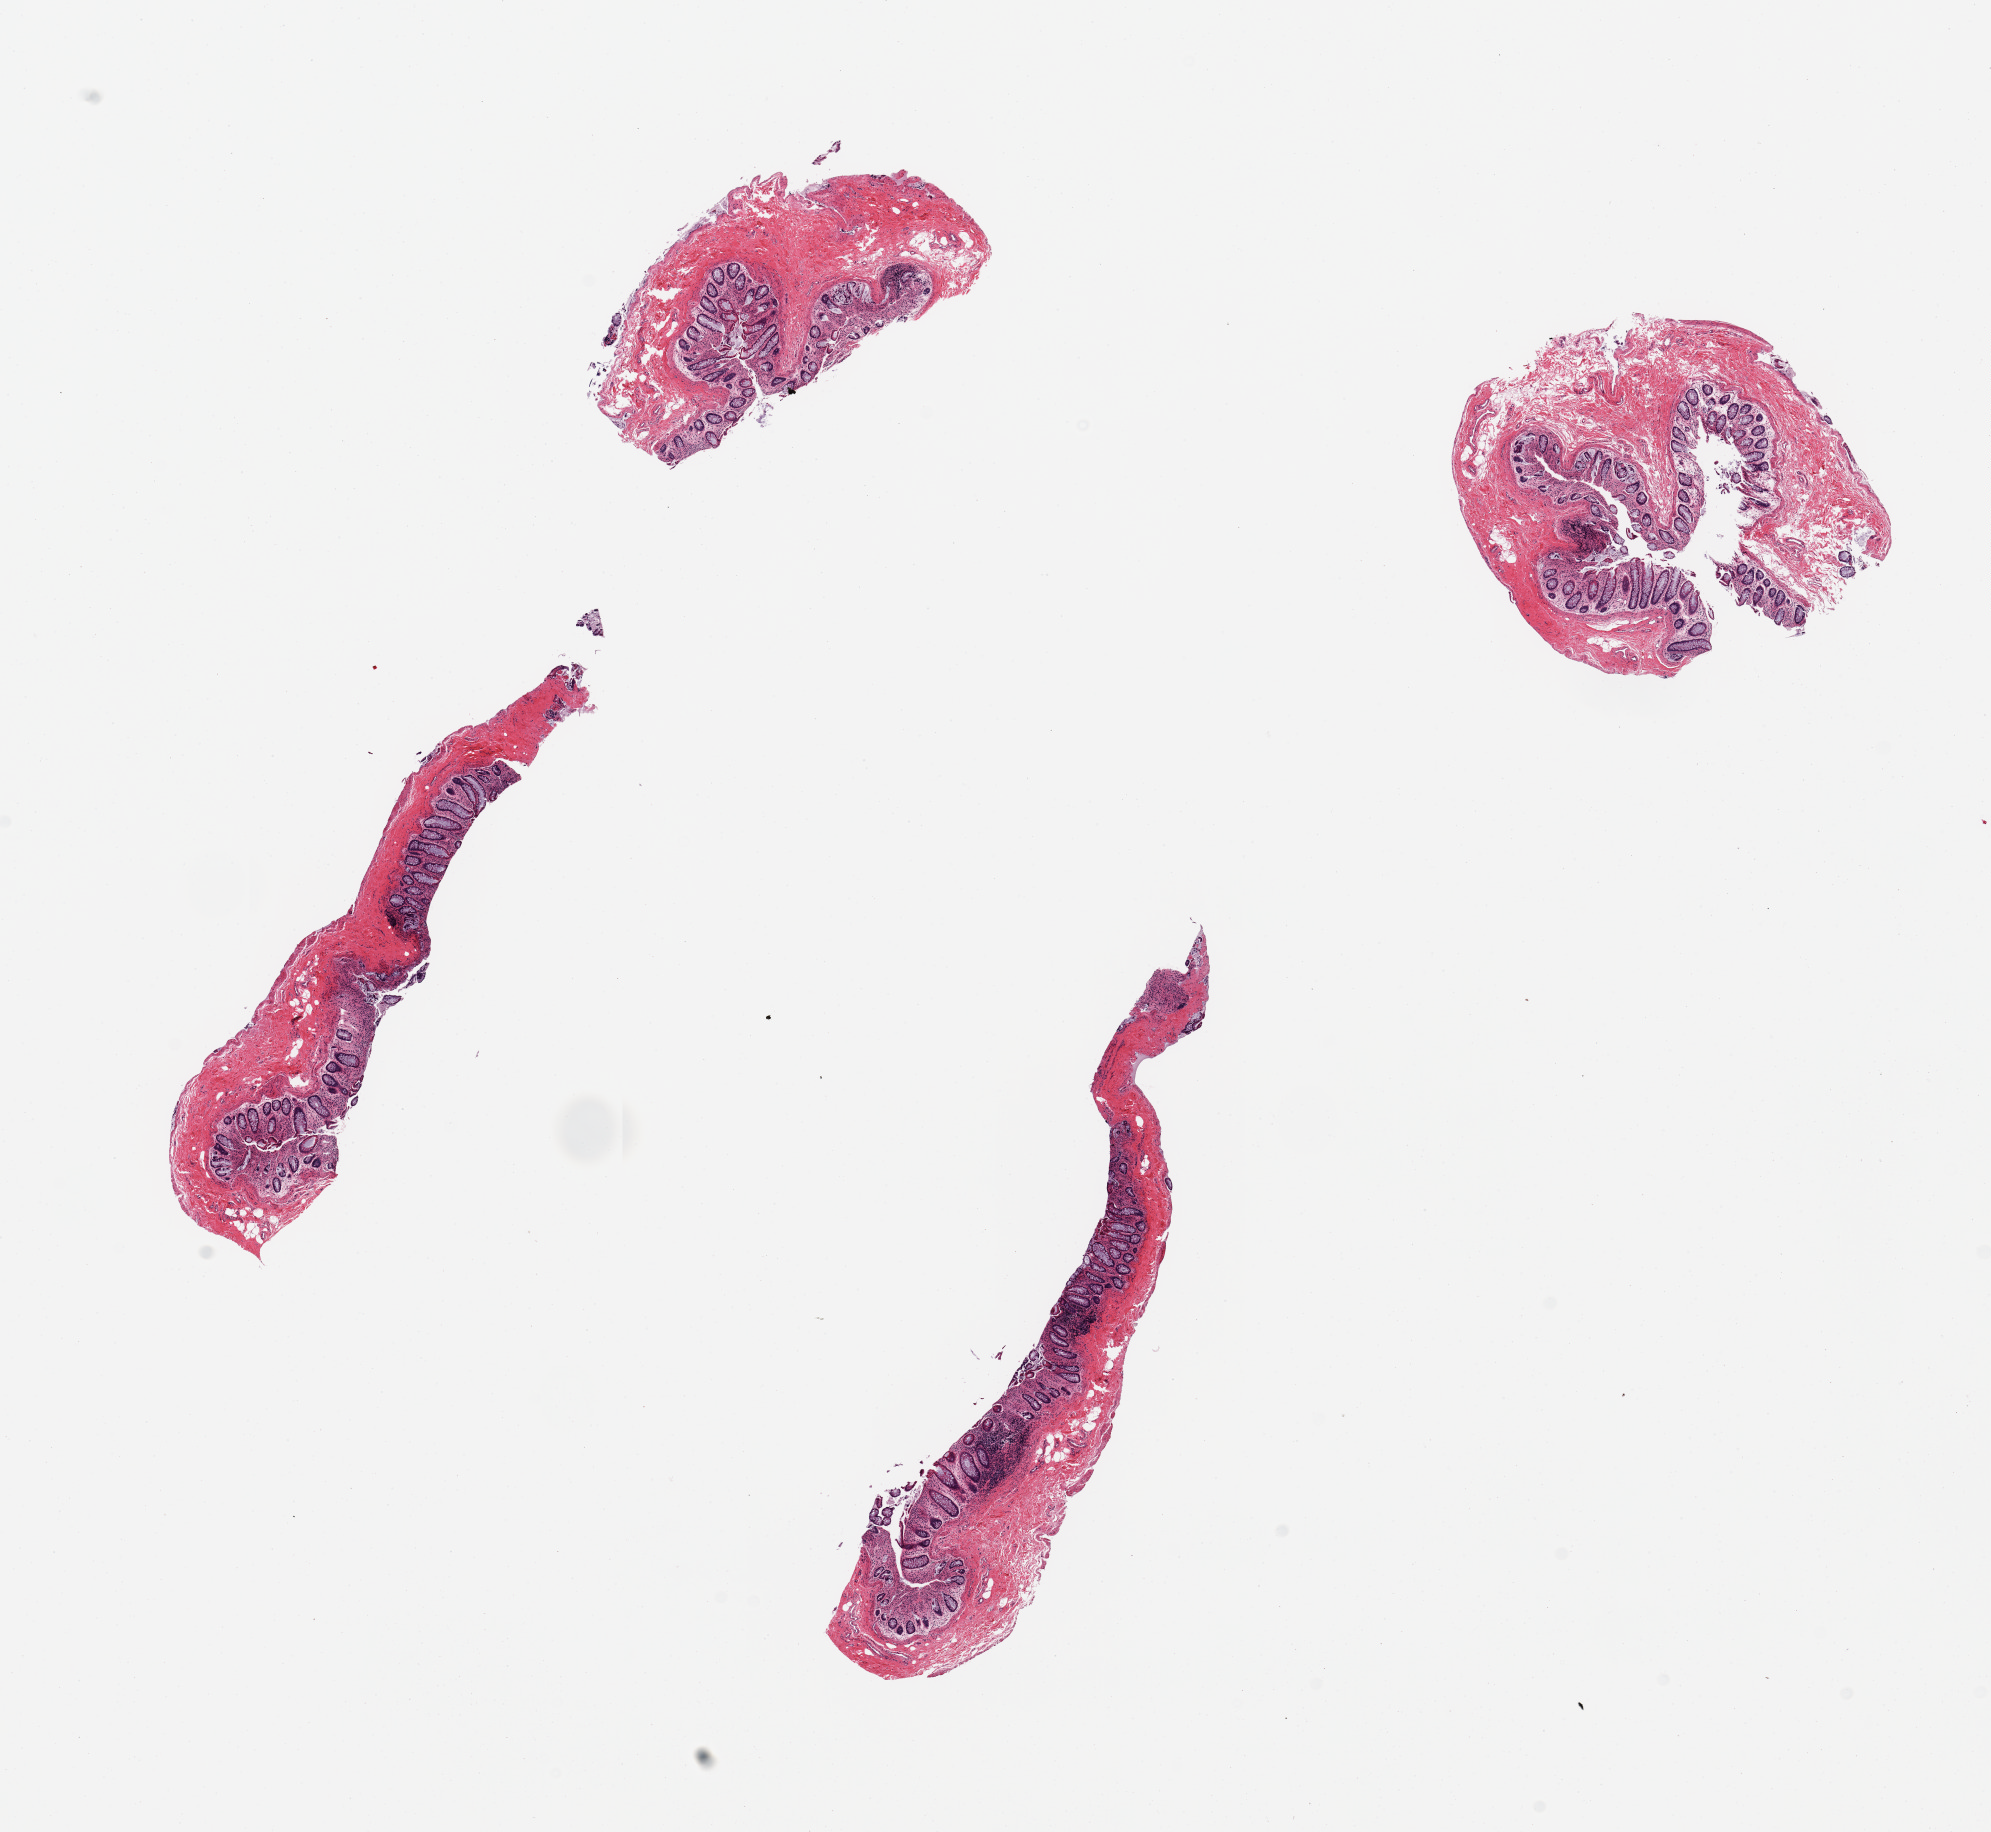
Whole-slide image, hematoxylin and eosin (H&E) stain — whole scanned area (about 15.8 x 14.5 mm) shown as a low-resolution overview, PAXgene-fixed paraffin-embedded (PFPE) section, section of sigmoid colon (target tissue), donor tissue sample. Female donor.
Review note (as recorded): 4 pieces; mild to moderately autolyzed mucosa (not target), minimal muscularis (target).